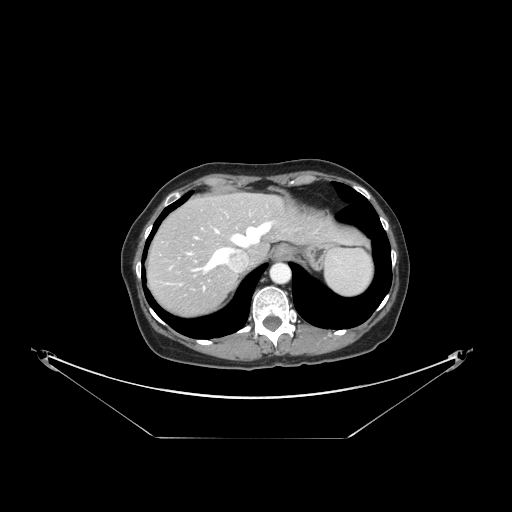
Contrast-enhanced abdominal CT, one axial slice. Position 123 of 148 along the scan axis. Intravenous contrast given. Soft-tissue window (W 400 / L 40 HU). 2.5 mm slice thickness. 512 × 512 image matrix, field of view 500 × 500 mm. Female patient, age 73 years. Case-level facts recorded for this patient, not image findings: diagnosis: colorectal cancer liver metastases, imaged before liver resection; multiple liver metastases: no; largest metastasis: 1 cm; disease in both lobes: no.
Annotated regions visible in this slice (outlined manually by an expert reader):
- hepatic veins: bounding box (x1, y1, x2, y2) in pixels: (195, 221, 274, 272)
- liver: (148, 195, 360, 315)
- planned liver remnant (the part of the liver to remain after resection): (175, 195, 359, 262)